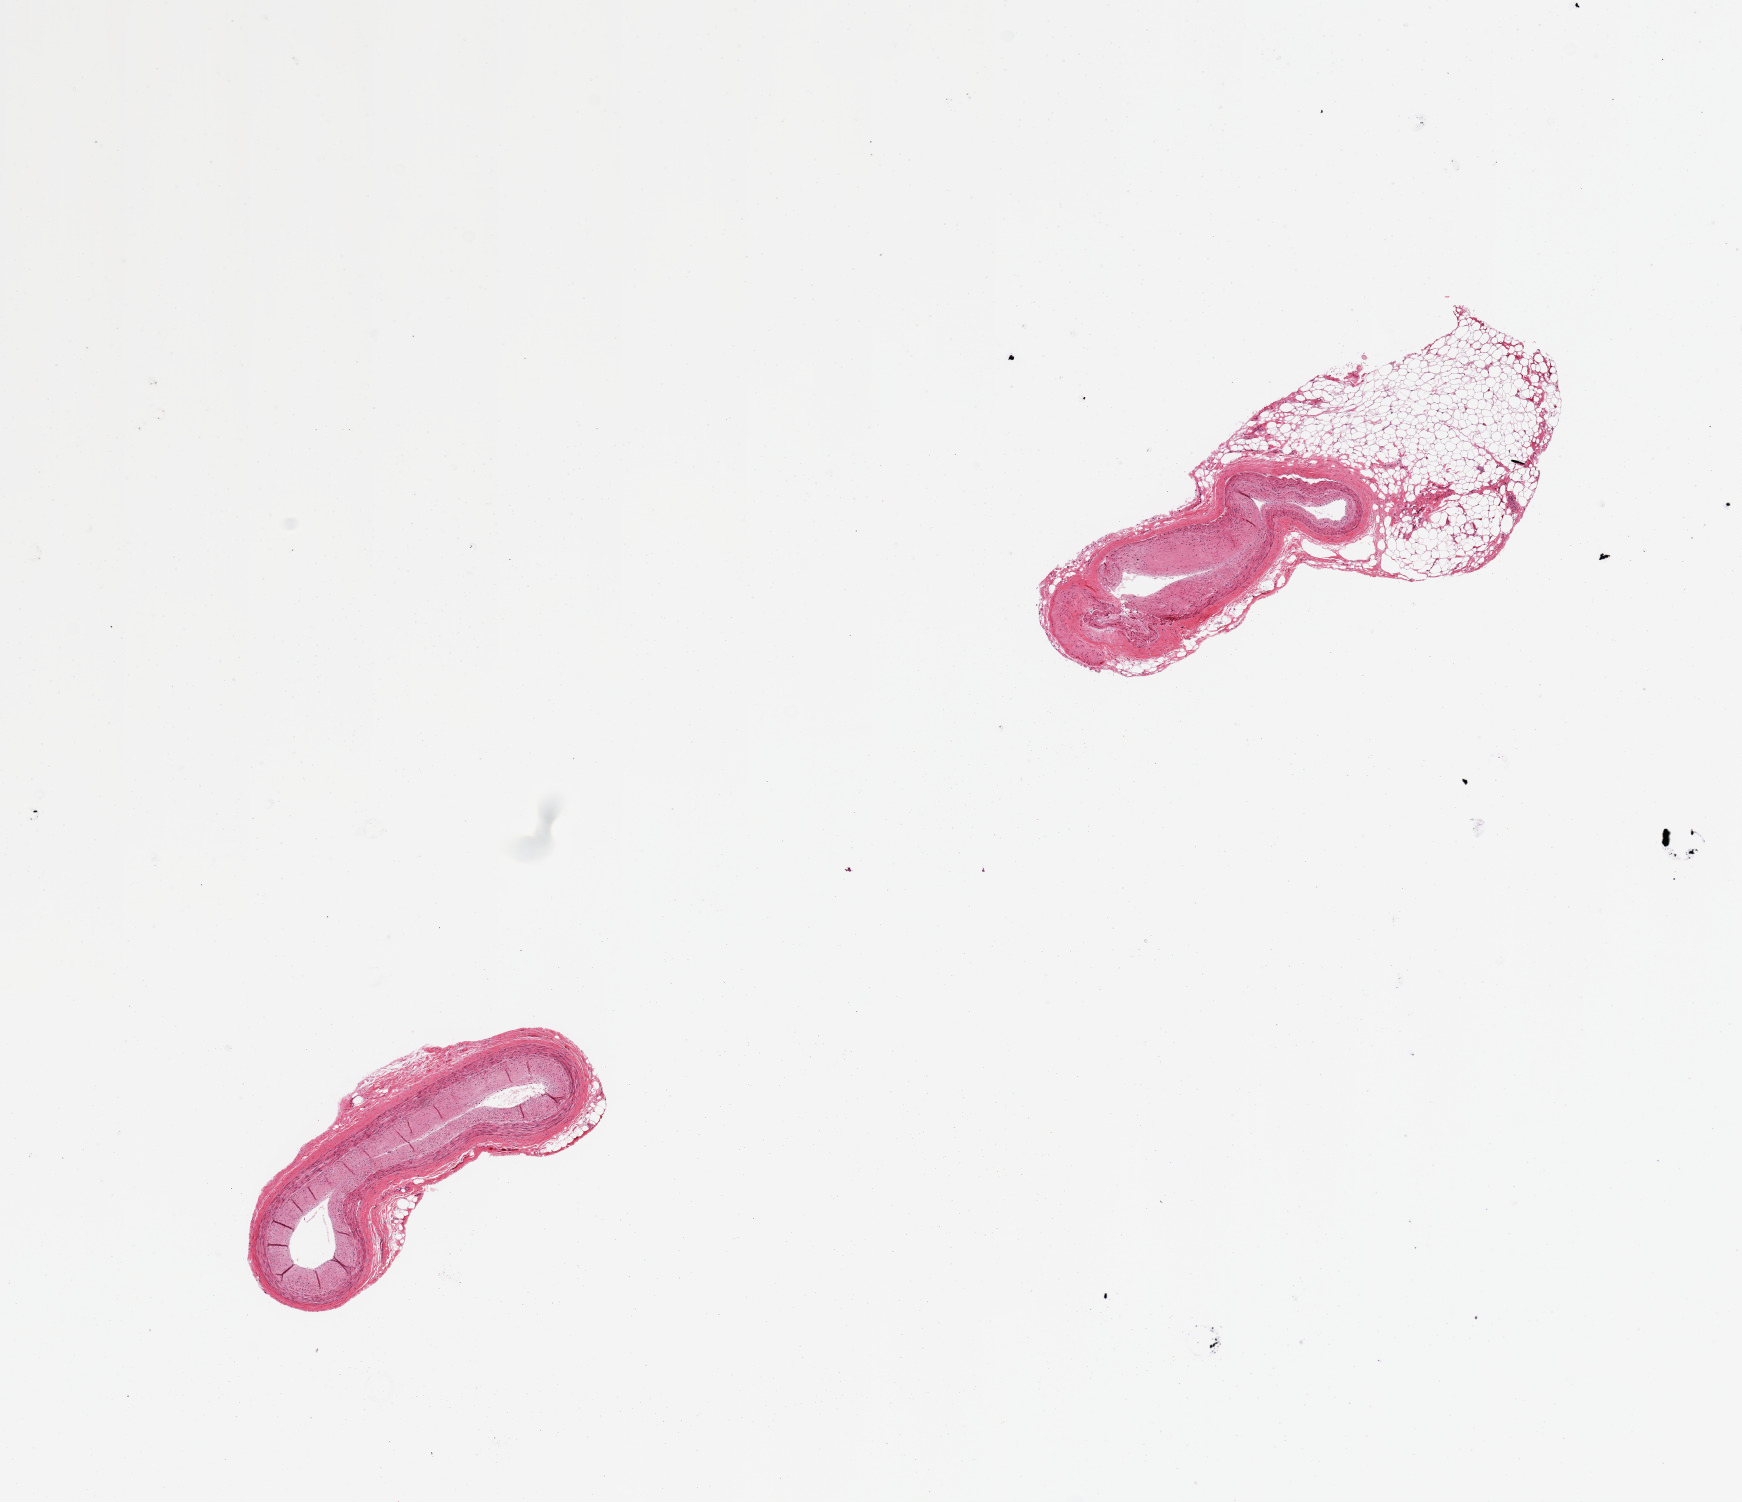
Hematoxylin and eosin (H&E) whole-slide image — whole scanned area (about 13.8 x 11.9 mm, from a 20x scan) shown as a low-resolution overview, PAXgene-fixed paraffin-embedded (PFPE) section, target tissue: coronary artery, donor tissue sample.
- review note (as recorded): 2 pieces, mild sclerosis, one piece includes 50% attachment of fat